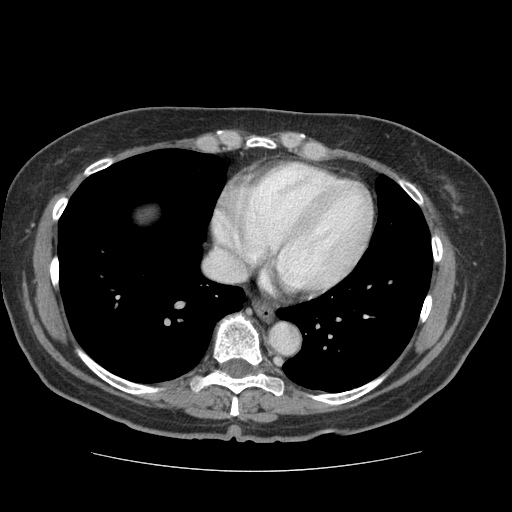
Contrast-enhanced abdominal CT (liver protocol), one axial slice. Position 72 of 75 along the scan axis. 140 kVp. Soft-tissue window (W 400 / L 40 HU). 2.5 mm slice thickness. 512 × 512 image matrix. From the clinical record (not read from this slice): diagnosis: hepatocellular carcinoma (patient treated with transarterial chemoembolisation; whether this scan precedes or follows treatment is not stated here); TNM stage (as recorded): Stage-I; Child-Pugh class: A; tumour nodularity: uninodular.
Outlined on this slice (semi-automatically segmented with operator editing):
- liver parenchyma outside the tumour (the mass and vessels are separate outlines, so this box may not span the whole liver): bounding box <136,204,158,223> (left, top, right, bottom; pixels)